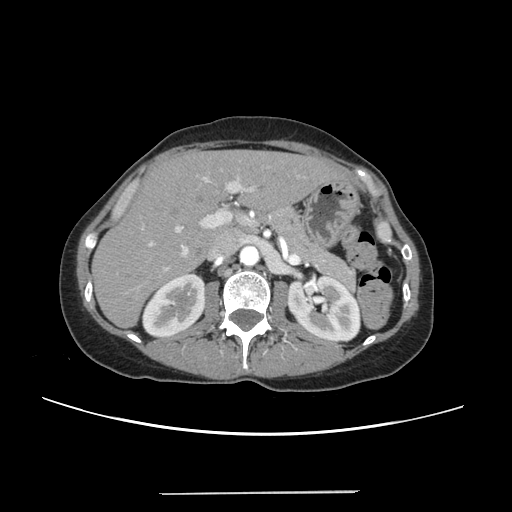
Contrast-enhanced abdominal CT, one axial slice. Slice 141 of 240 in the series (ordered by position). 120 kVp. Soft-tissue window (W 400 / L 40 HU). 512 × 512 image matrix. Female patient, age 60 years. From the clinical record (not read from this slice): diagnosis: colorectal cancer liver metastases, imaged before liver resection; multiple liver metastases: no; largest metastasis: 1.5 cm; disease in both lobes: no.
Annotated regions visible in this slice (manually delineated by an expert):
- liver: box from (x=94, y=151) to (x=343, y=326) px
- planned liver remnant (the part of the liver to remain after resection): (x=94, y=152)–(x=343, y=326)
- portal vein (with intrahepatic branches): (x=141, y=169)–(x=299, y=270)